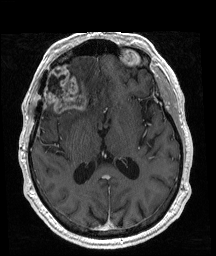
Brain MRI from a brain-tumour surgery series, one axial slice. Position 96 of 192 along the scan axis. T1-weighted post-contrast. 216 × 256 image matrix. From the clinical record (not read from this slice): histopathology: Glioblastoma; WHO grade: 4; IDH mutation: no; tumour location: Right Frontal.
Annotated regions visible in this slice (expert manual segmentation):
- previous resection cavity: bounding box [x1, y1, x2, y2] px = [48, 76, 64, 96]